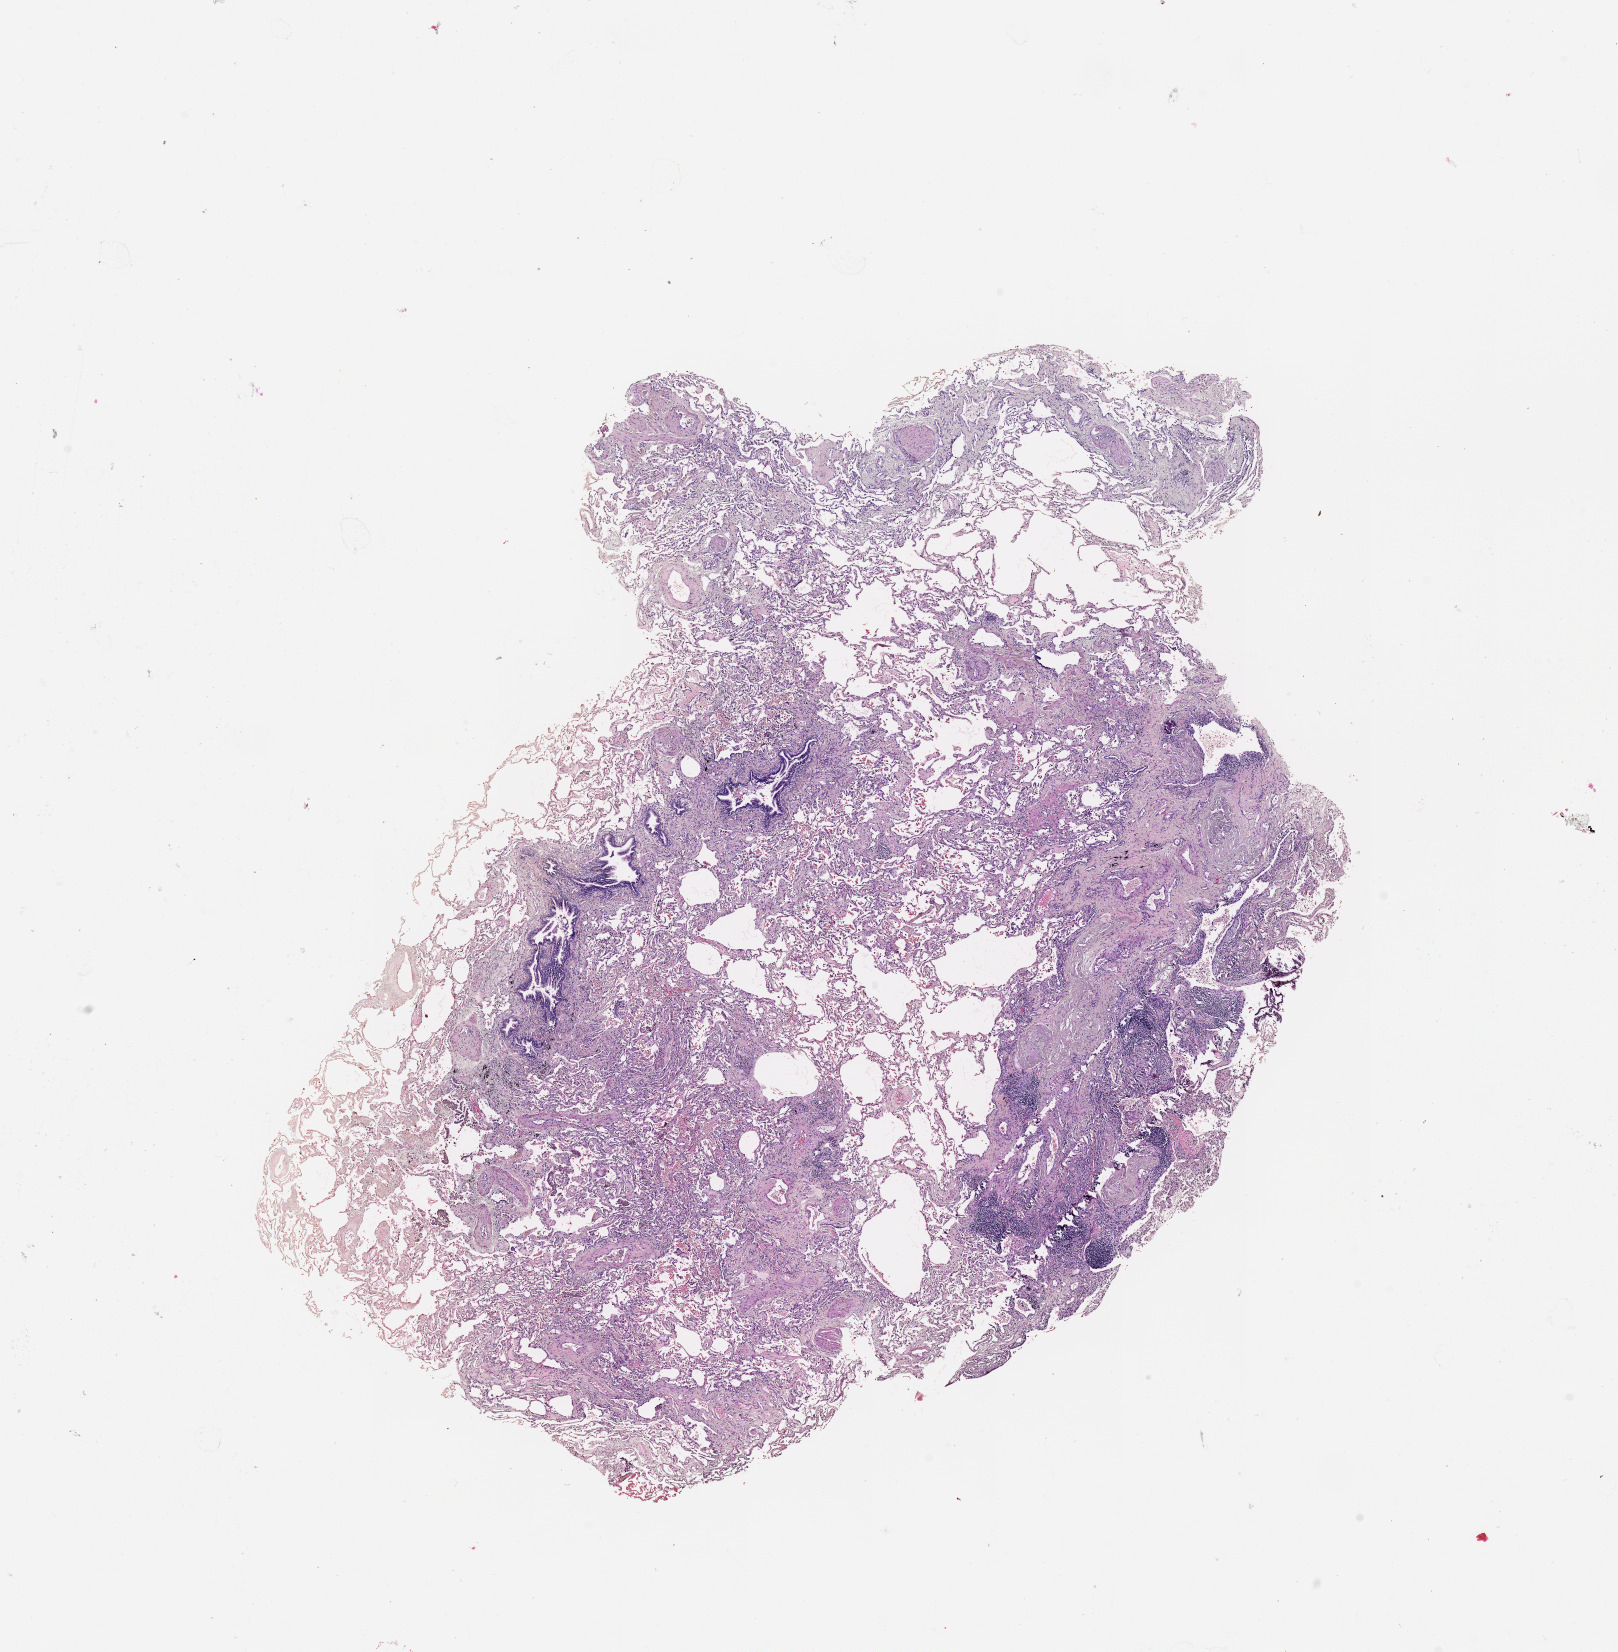
Whole-slide histology image, H&E-stained — low-resolution overview of the scanned area, about 13.0 x 13.3 mm (acquisition: 20x scan), normal (non-tumour) tissue sample, sampled site: lung. 68-year-old male patient.
- this section: normal (non-tumour) tissue from the same patient
- patient diagnosis: Adenocarcinoma, NOS